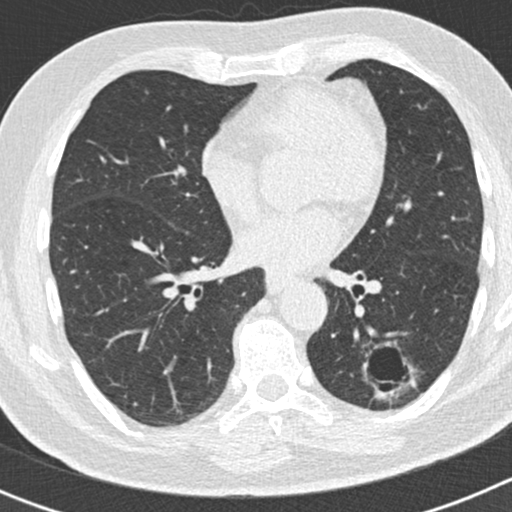
Low-dose screening chest CT, axial slice. Second annual screen. Lung window (W 1500 / L -600 HU). 2 mm slice thickness. Standard (soft-tissue) reconstruction kernel (B30f). Slice 93 of 186 in the series. 512 × 512 image matrix. Male participant, aged 66 years at enrolment. Former smoker at enrolment.
Expert reader's lesion annotation, bounding box <349,333,413,406> (left, top, right, bottom; pixels). The exam's reader record, not a measurement of the box and not confirmed to be the same lesion: non-calcified nodule or mass ≥4 mm, left lower lobe, 50 × 33 mm, smooth margins, pre-existing on the prior screen: yes; interval growth: yes. Official screen result: positive, other. Participant outcome: lung cancer diagnosed 440 days after this screen — adenocarcinoma, NOS, left lower lobe, poorly differentiated (G3), stage IB (AJCC 6th edition), 38 mm at pathology.